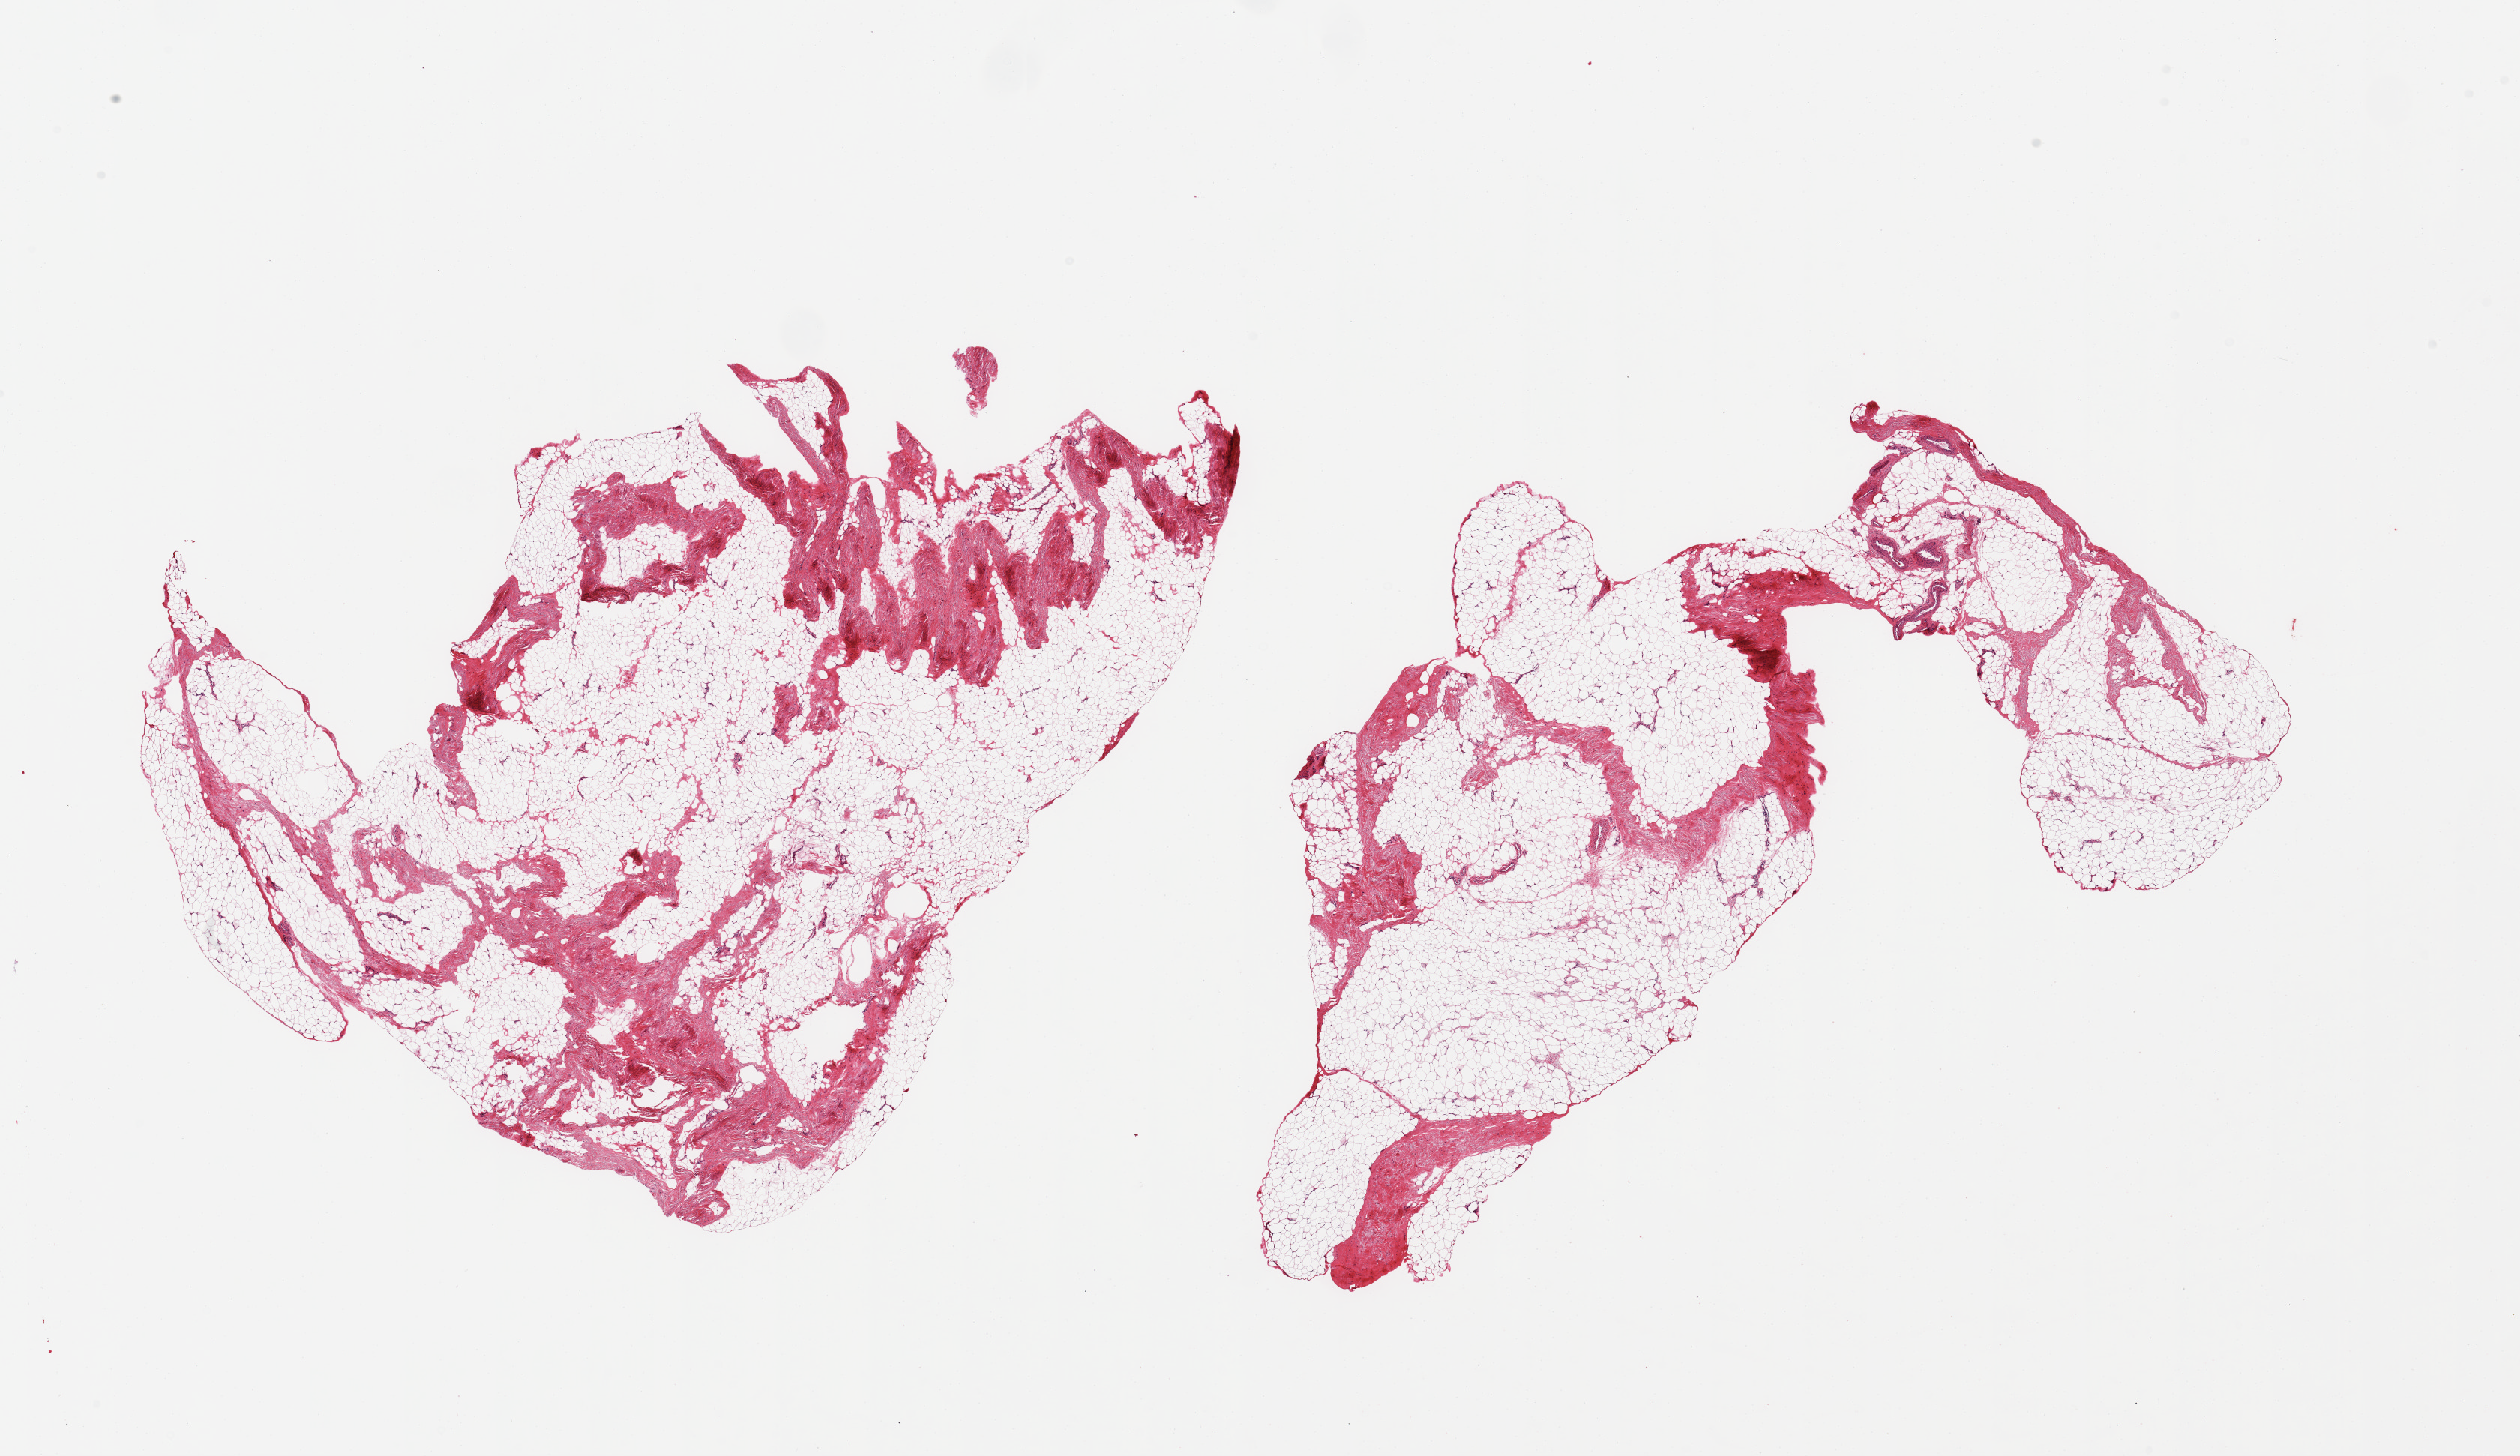
Whole-slide image, haematoxylin and eosin stain, low-resolution overview of the scanned area, about 26.6 x 15.4 mm. PAXgene-fixed, paraffin-embedded tissue. Section of adipose tissue (target tissue). Tissue donor sample. Donor: male.
Reviewer comment on this tissue sample: 2 pieces; 10% & 20% fibrous content.